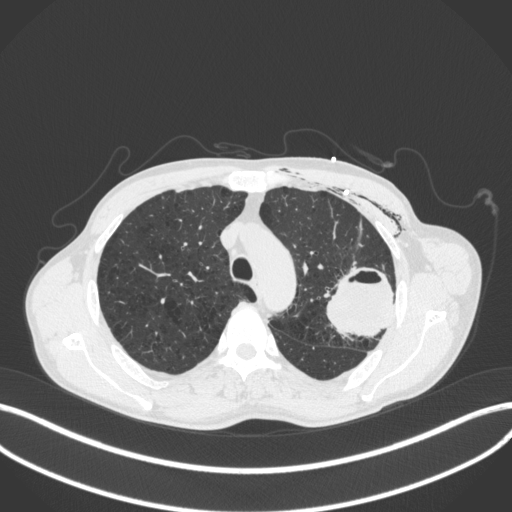
Chest CT, one axial slice; slice 301 of 416 in the series (ordered by position); reconstruction kernel B31f; lung window (W 1500 / L -600 HU); 512 × 512 image matrix, field of view 400 × 400 mm. Male patient, age 58 years. Case-level facts recorded for this patient, not image findings: clinical TNM (as recorded): T3 N0 M0.
Structures marked on this image (bounding box drawn by a radiologist):
- lung tumour (recorded histology: adenocarcinoma): bounding box [x1, y1, x2, y2] px = [322, 263, 402, 343]